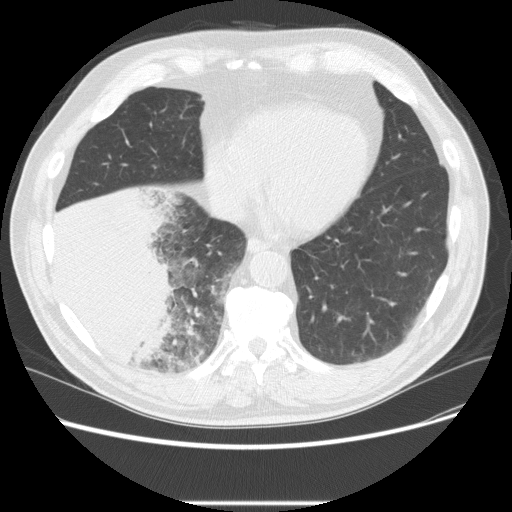
Low-dose screening chest CT, one axial slice; position 70 of 233 along the scan axis; reconstruction kernel STANDARD; 120 kVp; lung window (W 1500 / L -600 HU); 2.5 mm slice thickness; 512 × 512 image matrix, field of view 380 × 380 mm.
Annotated regions visible in this slice (manually delineated by an expert):
- lesion 3 (tumor, lower lobe of right lung): bounding box [x1, y1, x2, y2] px = [51, 189, 177, 367]